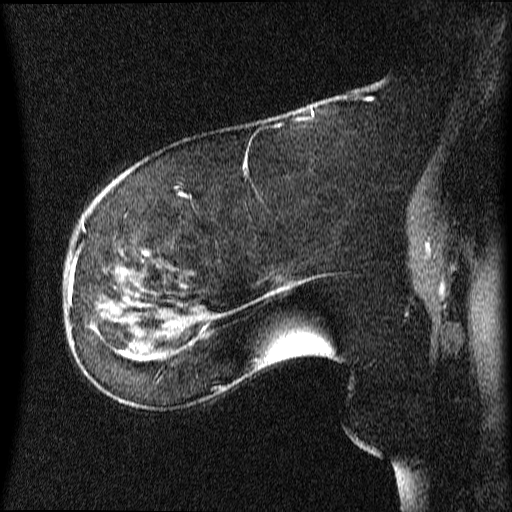
Breast MRI (dynamic contrast-enhanced), one sagittal slice; slice 22 of 64 in the series (ordered by position); dynamic contrast-enhanced series, image 2 of 4 at this slice position (ordered by acquisition); 1.5 T; TE 4.2 ms, TR 9 ms; 2 mm slice thickness; 512 × 512 image matrix, field of view 200 × 200 mm. Female patient, age 63 years.
Annotated regions visible in this slice (semi-automatic segmentation, software-assisted and operator-edited):
- analysis volume of interest (the breast-tissue region the enhancement analysis was run in; not a lesion): bounding box <66,272,131,353> (left, top, right, bottom; pixels)
- tumour enhancement mask (voxels above the 70 % enhancement threshold inside the analysis volume of interest): <68,272,130,353>